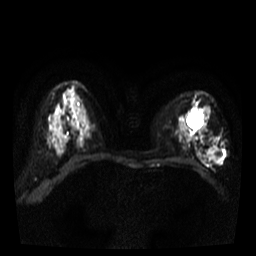
Breast MRI, one axial slice. Slice 24 of 38 in the series (ordered by position). Diffusion-weighted series; image 2 of 4 stored at this slice position (different b-values; order by instance number). 3 T. 5 mm slice thickness. 256 × 256 image matrix. Female patient.
Structures marked on this image (manually delineated by an expert):
- tumour on diffusion-weighted imaging: bounding box <208,147,218,163> (left, top, right, bottom; pixels)